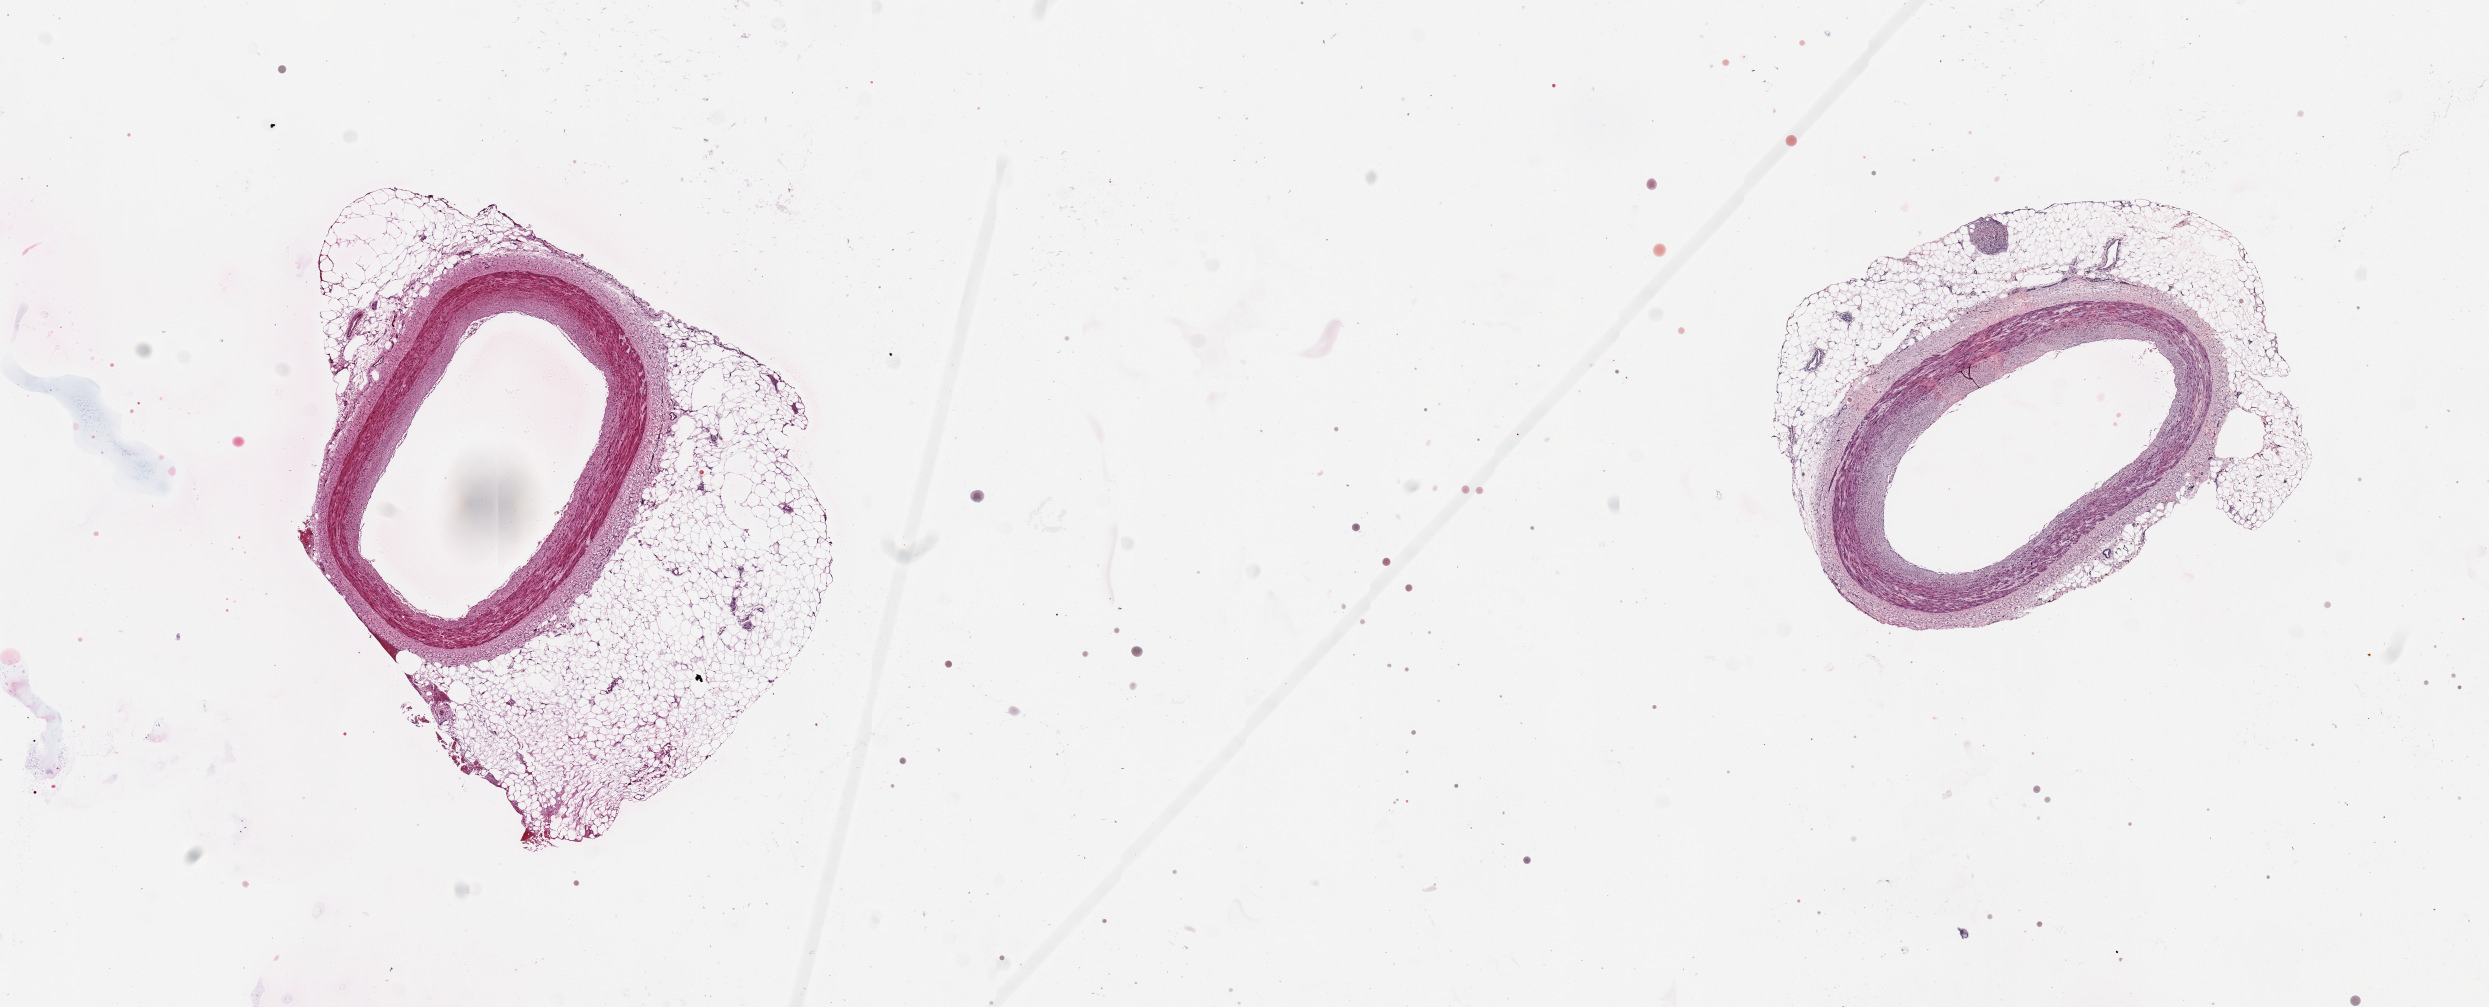
H&E whole-slide image — a low-resolution overview of the entire scanned area, about 19.7 x 8.0 mm (from a 20x scan), PAXgene-fixed, paraffin-embedded tissue, sampled site (target tissue): coronary artery, donor tissue sample. Donor sex: male.
• pathologist's review note for this sample: 2 pieces, 4x3.5 & 5x4mm; 3mm arteries with up to 1.6 mm surrounding adipose